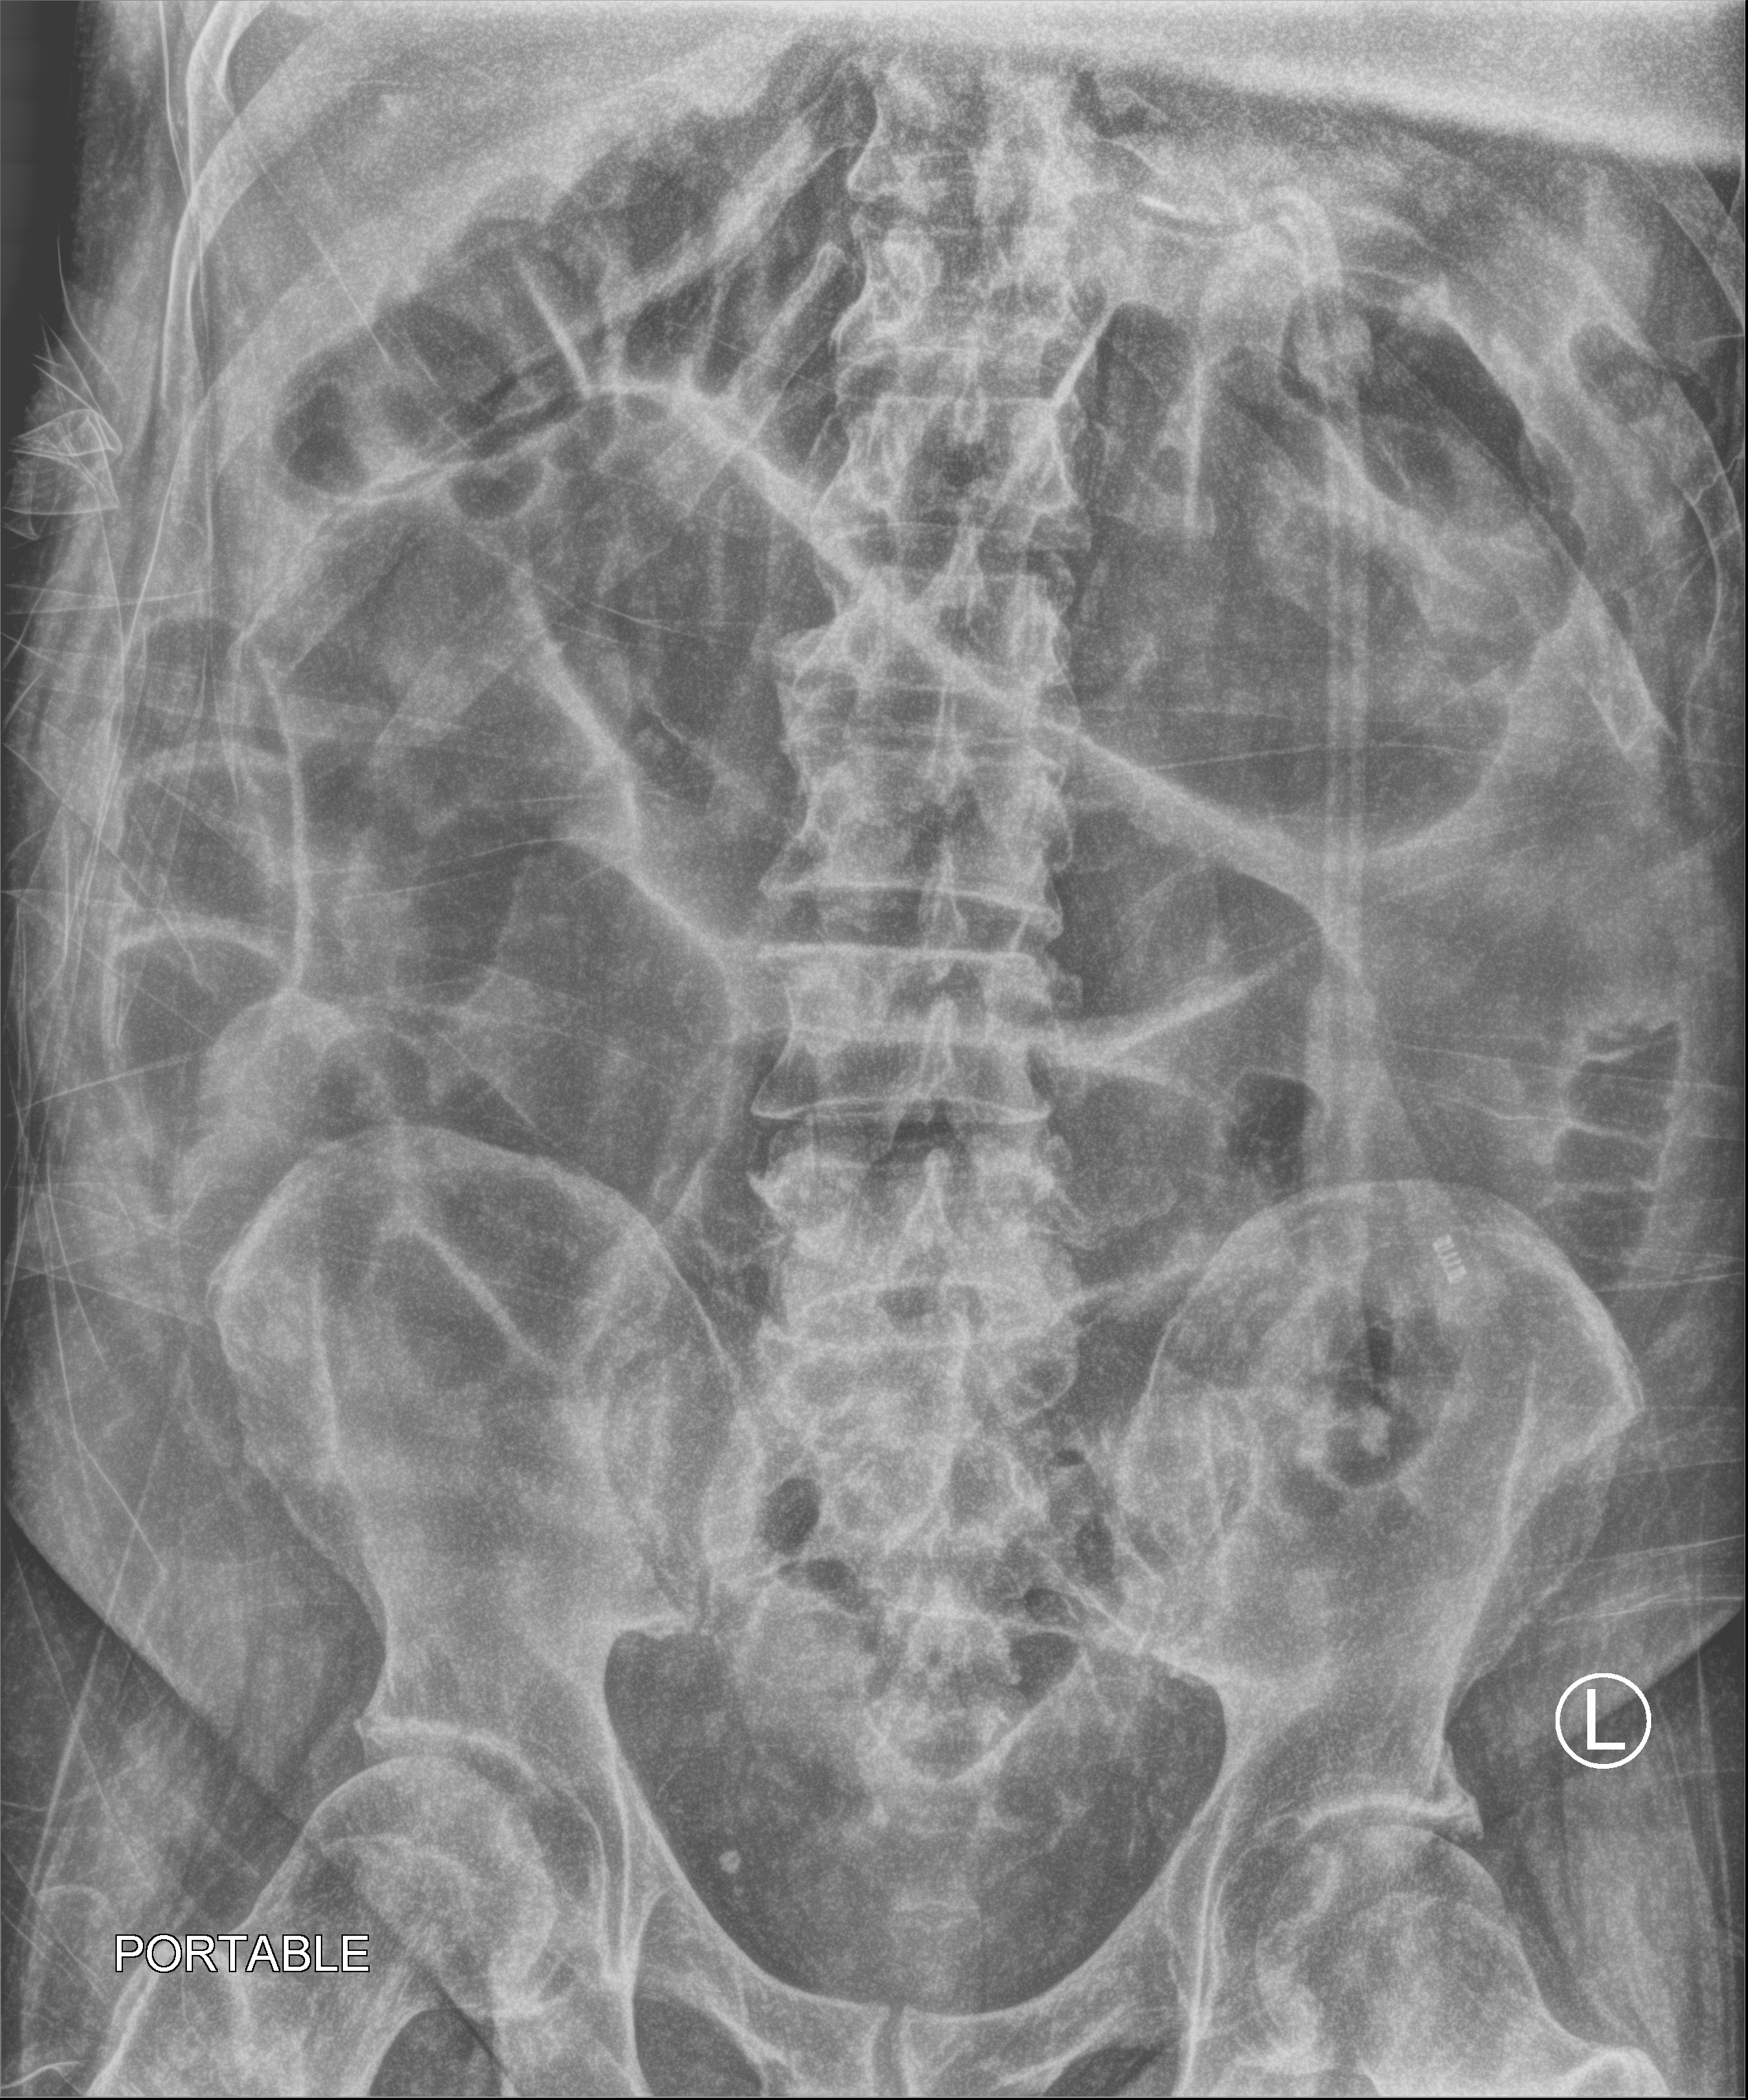
Abdomen X-ray (portable); anteroposterior (AP) projection. Male patient hospitalised with COVID-19, age 60–74 years.
Hospital-stay facts (about this admission, not read from this image; timing relative to this image not recorded):
- mechanically ventilated during this hospital stay: no
- admitted to intensive care during this hospital stay: no
- length of hospital stay: 5 days